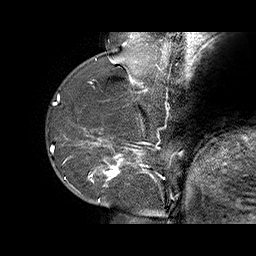
Breast MRI (dynamic contrast-enhanced), one sagittal slice. Slice 17 of 70 in the series (ordered by position). Dynamic contrast-enhanced series, time point 2 of 6 at this slice position (early post-contrast). 1.5 T. TE 4.5 ms, TR 32.4 ms. 256 × 256 image matrix, field of view 180 × 180 mm. Female patient. Case-level facts recorded for this patient, not image findings: setting: breast cancer imaged before/during neoadjuvant chemotherapy; receptor status: HR-positive, HER2-negative.
Annotated regions visible in this slice (semi-automatically segmented with operator editing):
- analysis volume of interest (the breast-tissue region the enhancement analysis was run in; not a lesion): box from (x=71, y=128) to (x=159, y=202) px
- tumour enhancement mask (voxels above the 100 % enhancement threshold inside the analysis volume of interest): (x=78, y=128)–(x=156, y=202)